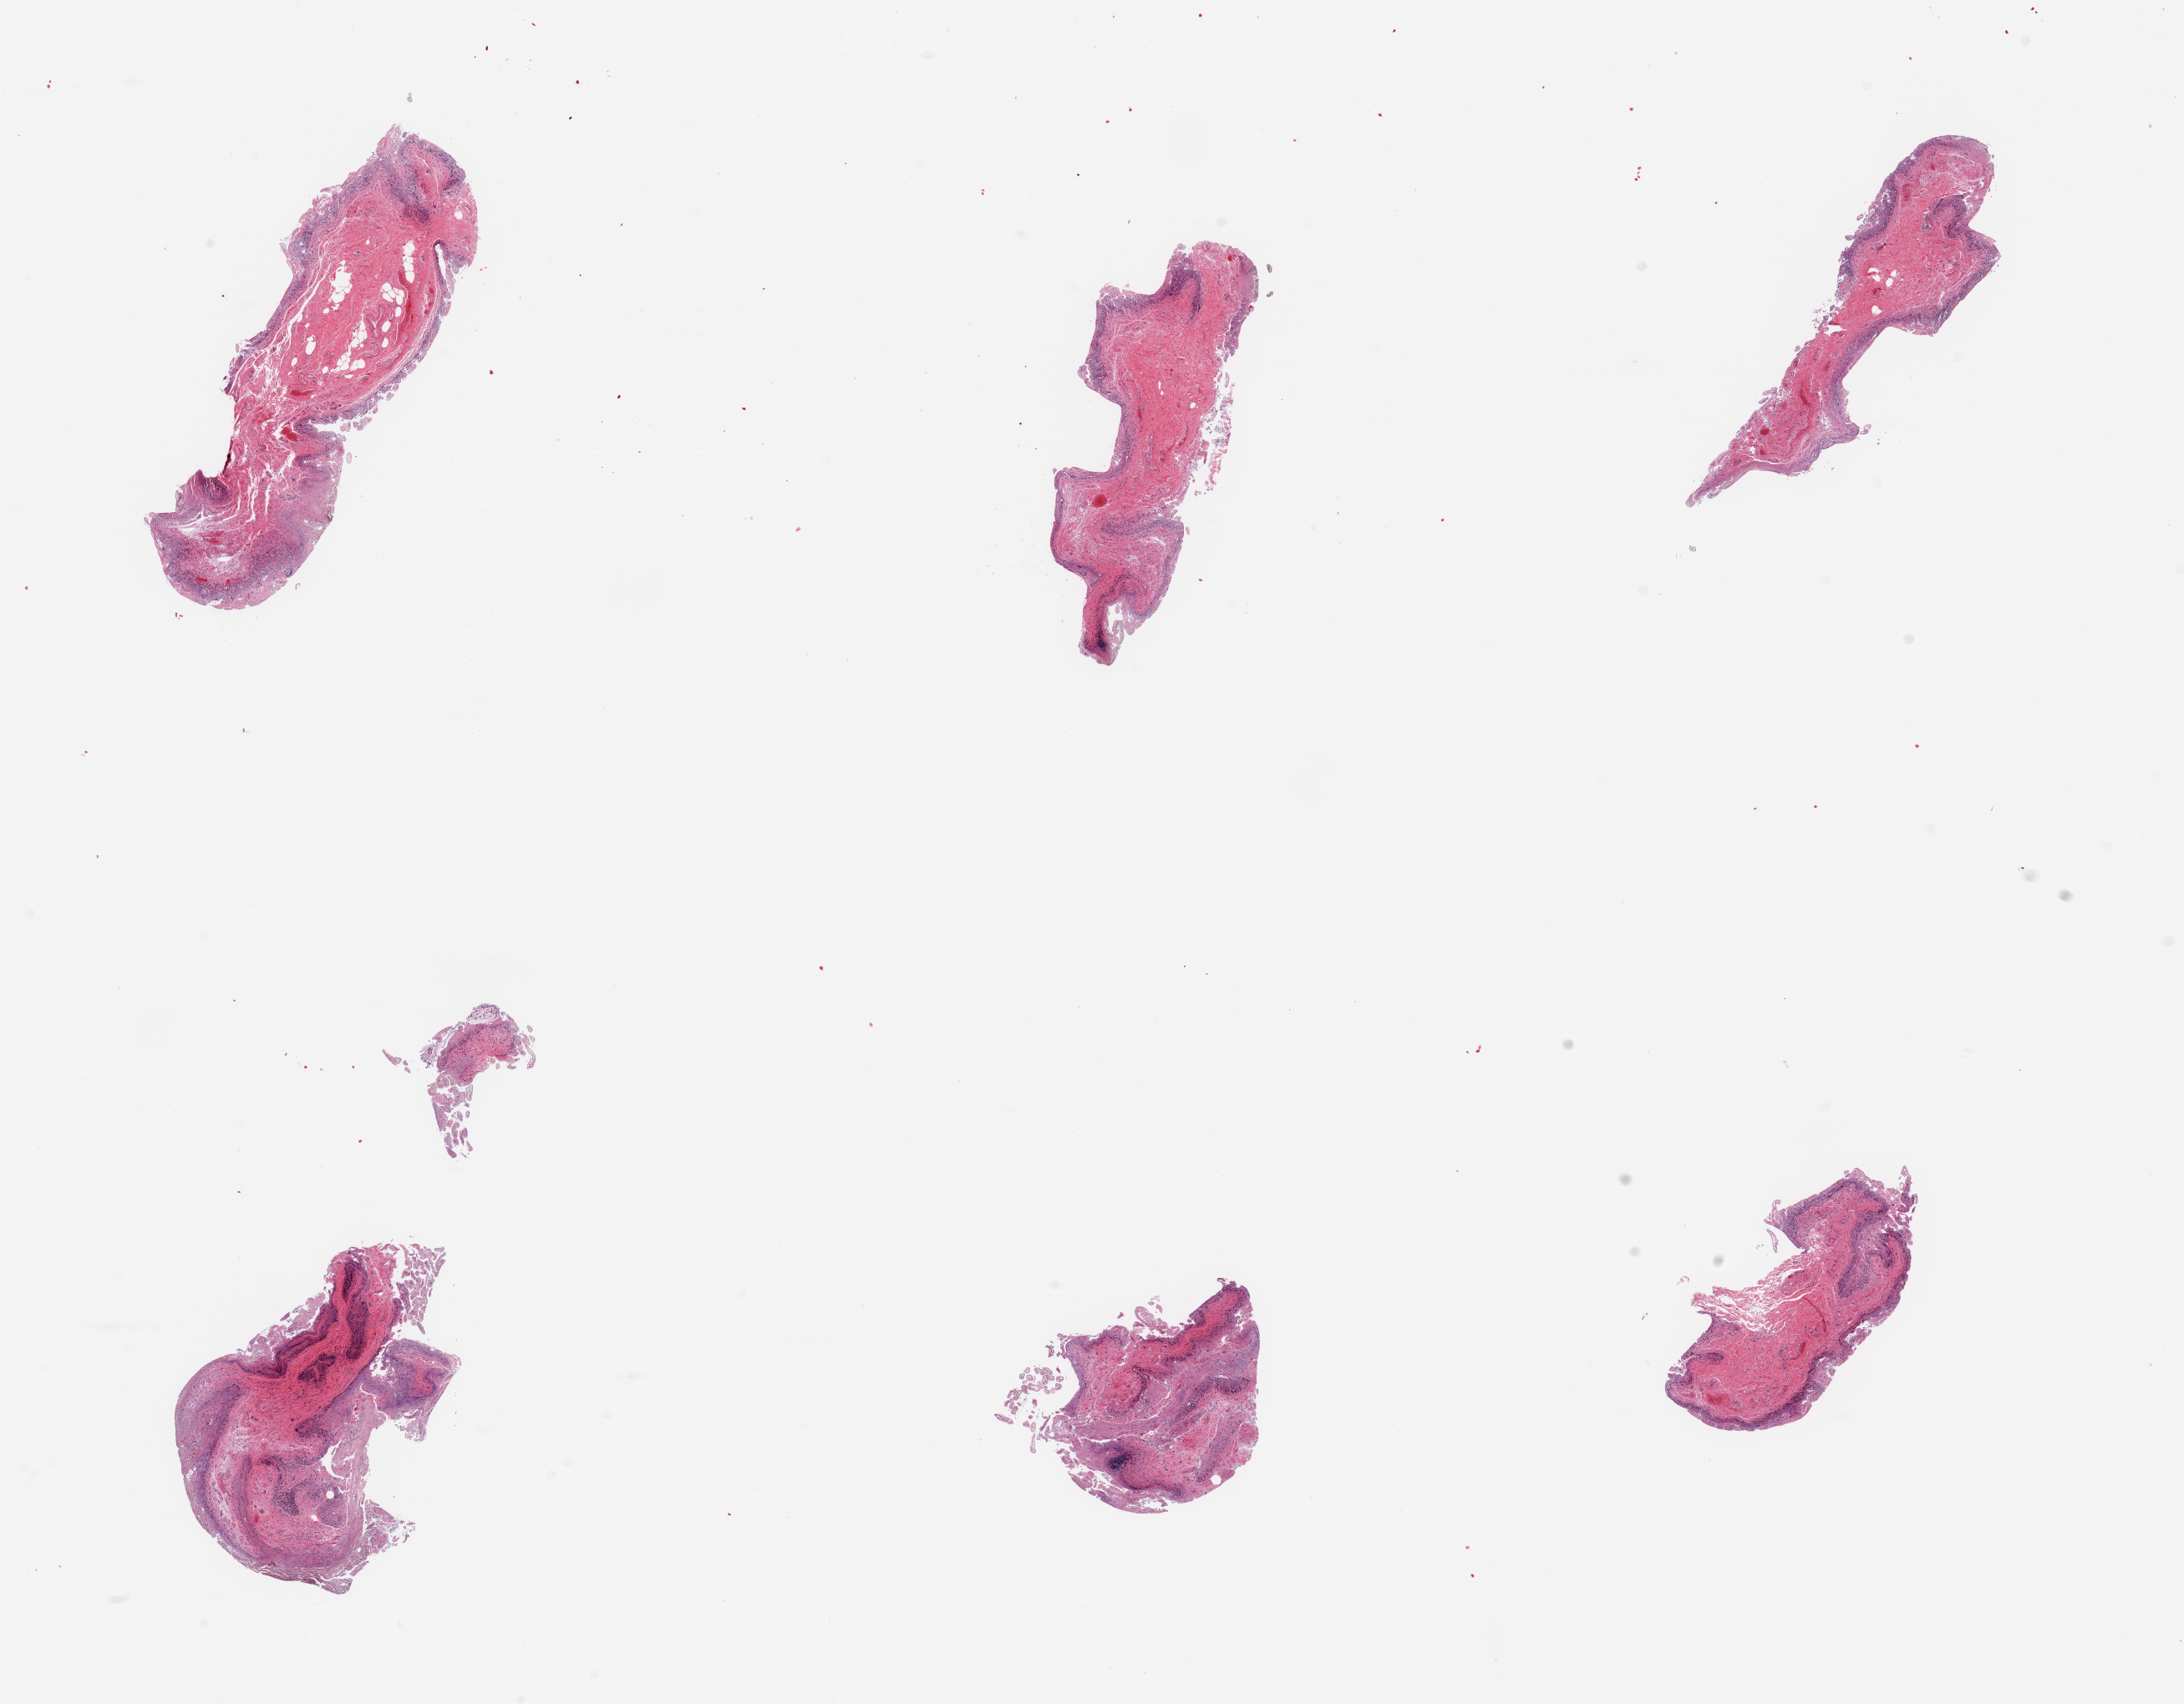
Whole-slide image, haematoxylin and eosin stain, whole scanned area (about 20.7 x 16.1 mm) shown as a low-resolution overview. PAXgene-fixed, paraffin-embedded tissue. Sampled site (target tissue): ileum. Tissue donor sample. Donor sex: male.
• reviewer comment on this tissue sample: 6 pieces, only trace lymphoid aggregates